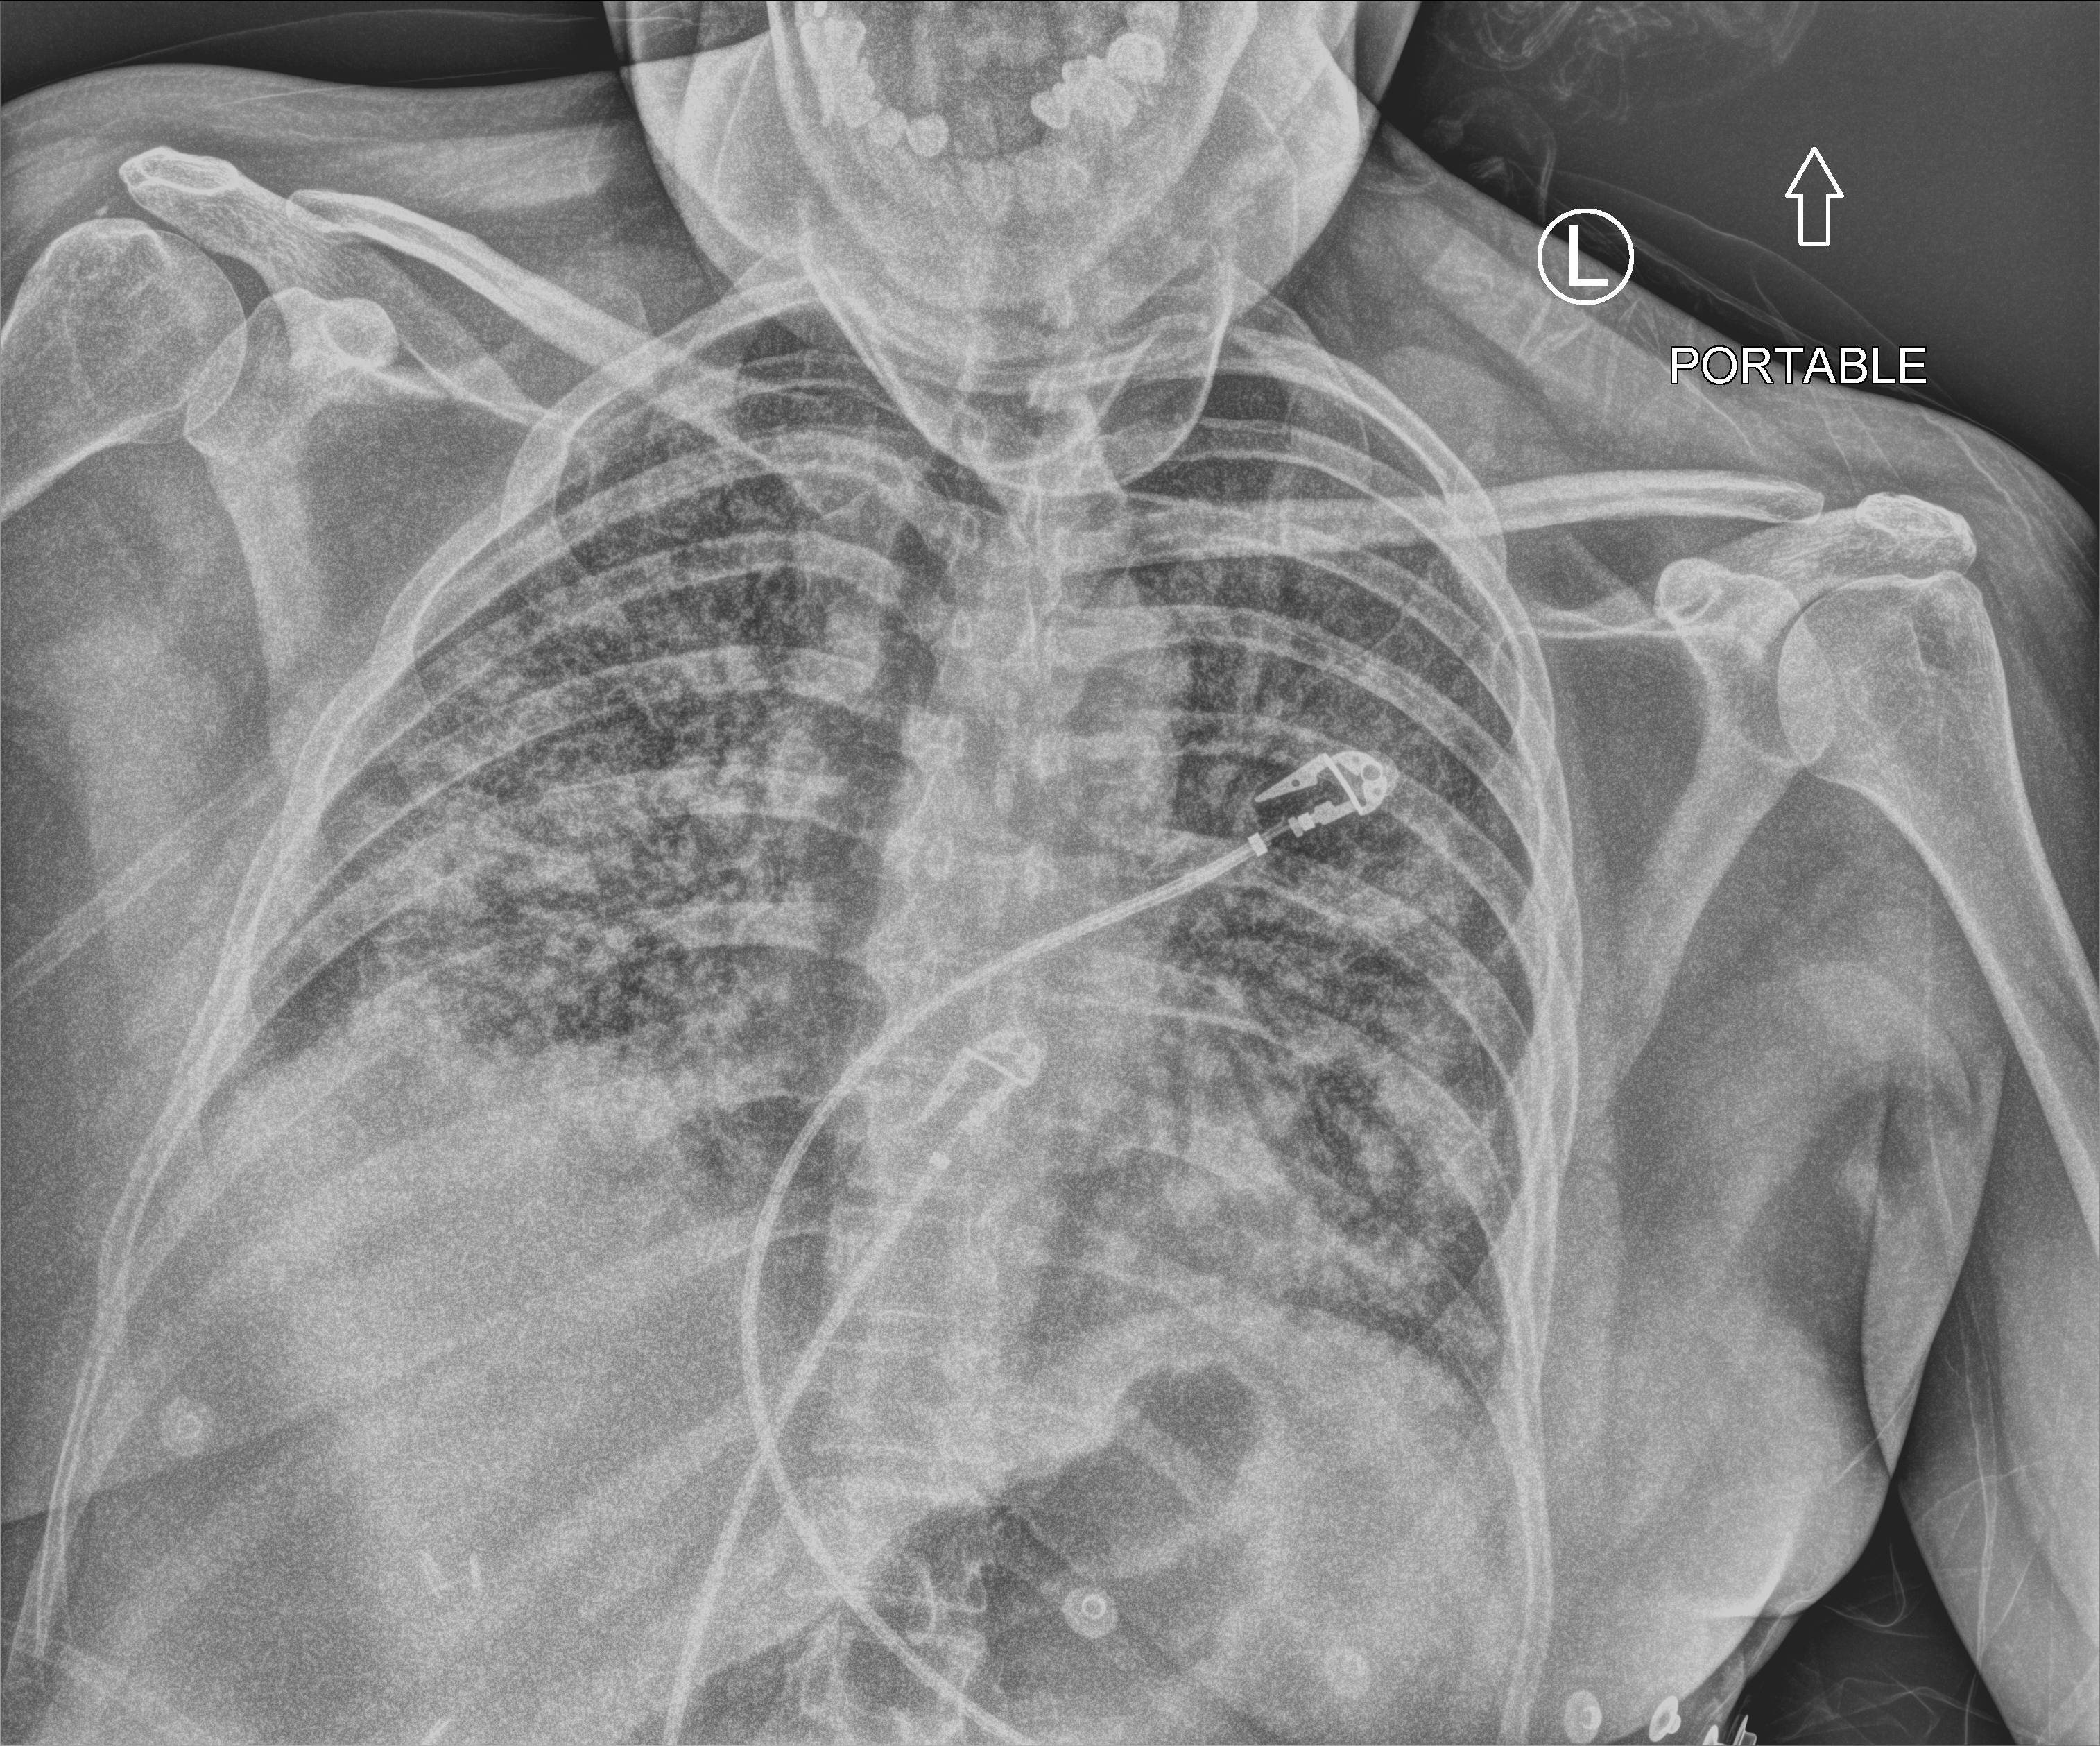
Chest X-ray (portable), anteroposterior (AP) projection. Female patient hospitalised with COVID-19, age 18–59 years.
Admission-level facts for this patient (not findings on this image; timing relative to this image not recorded): mechanically ventilated during this hospital stay: no; admitted to intensive care during this hospital stay: no.